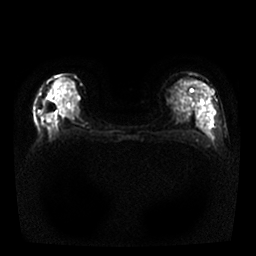
Breast MRI, one axial slice; slice 11 of 25 in the series (ordered by position); diffusion-weighted series; image 2 of 4 stored at this slice position (different b-values; order by instance number); 1.5 T; 4 mm slice thickness; 256 × 256 image matrix, field of view 330 × 330 mm. Female patient.
Outlined on this slice (outlined manually by an expert reader):
- tumour on diffusion-weighted imaging: box from (x=46, y=113) to (x=54, y=119) px